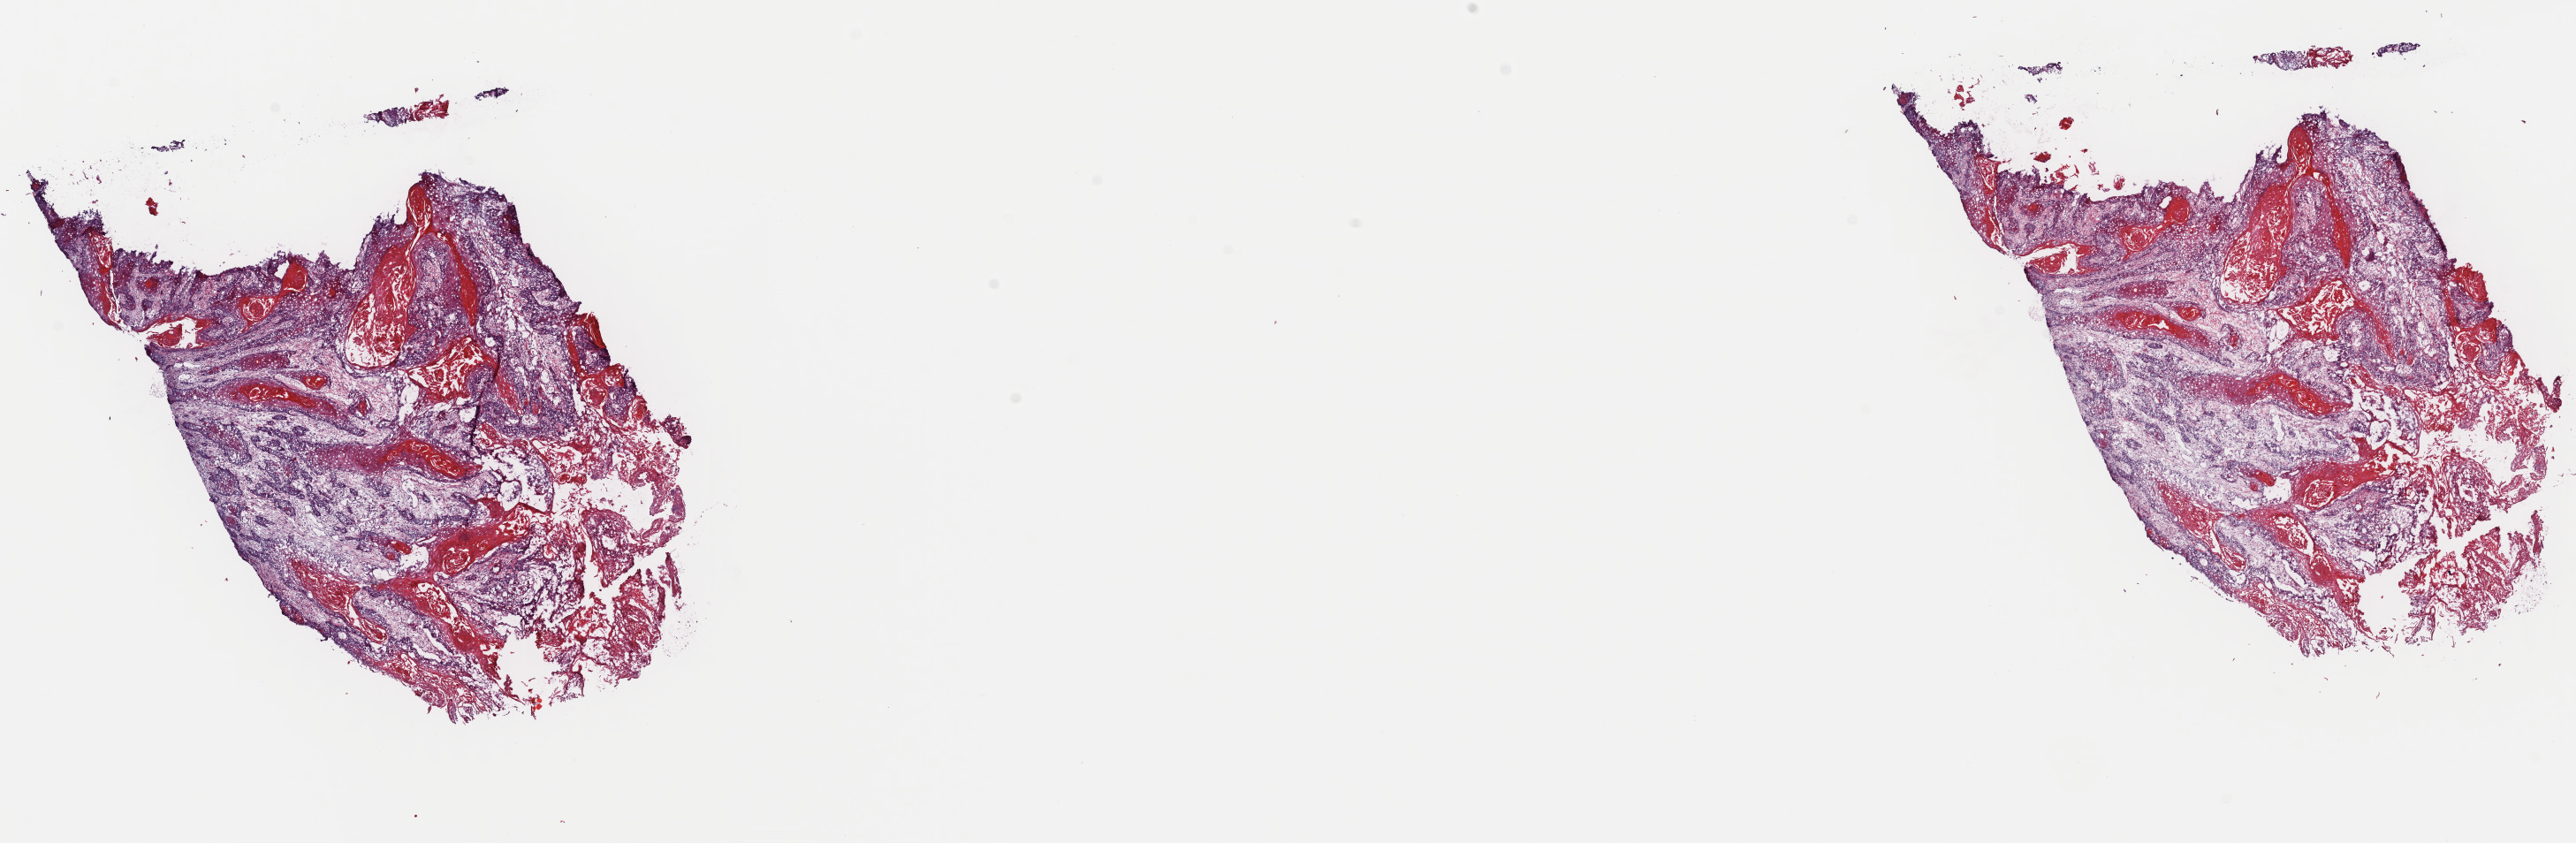
Whole-slide histology image, H&E-stained — low-resolution overview of the scanned area, about 23.0 x 7.5 mm (acquisition: 40x scan); frozen section from the top of the tissue portion; head and neck, primary tumour sample. Female, age 72 years at initial diagnosis. Histologic grade: G1 (well differentiated). Pathologist review of this section (percent, as recorded): tumour cells 70%, tumour nuclei 80%, normal cells 0%, stromal cells 30%, necrosis 0%. Infiltration values recorded for this section: lymphocyte infiltration 10%, monocyte infiltration 0%, neutrophil infiltration 0%.
TNM: T2 N0 M0. Pathologic diagnosis: Squamous cell carcinoma, keratinizing, NOS (tongue, NOS). Laterality: right. AJCC pathologic stage: II (7th edition).